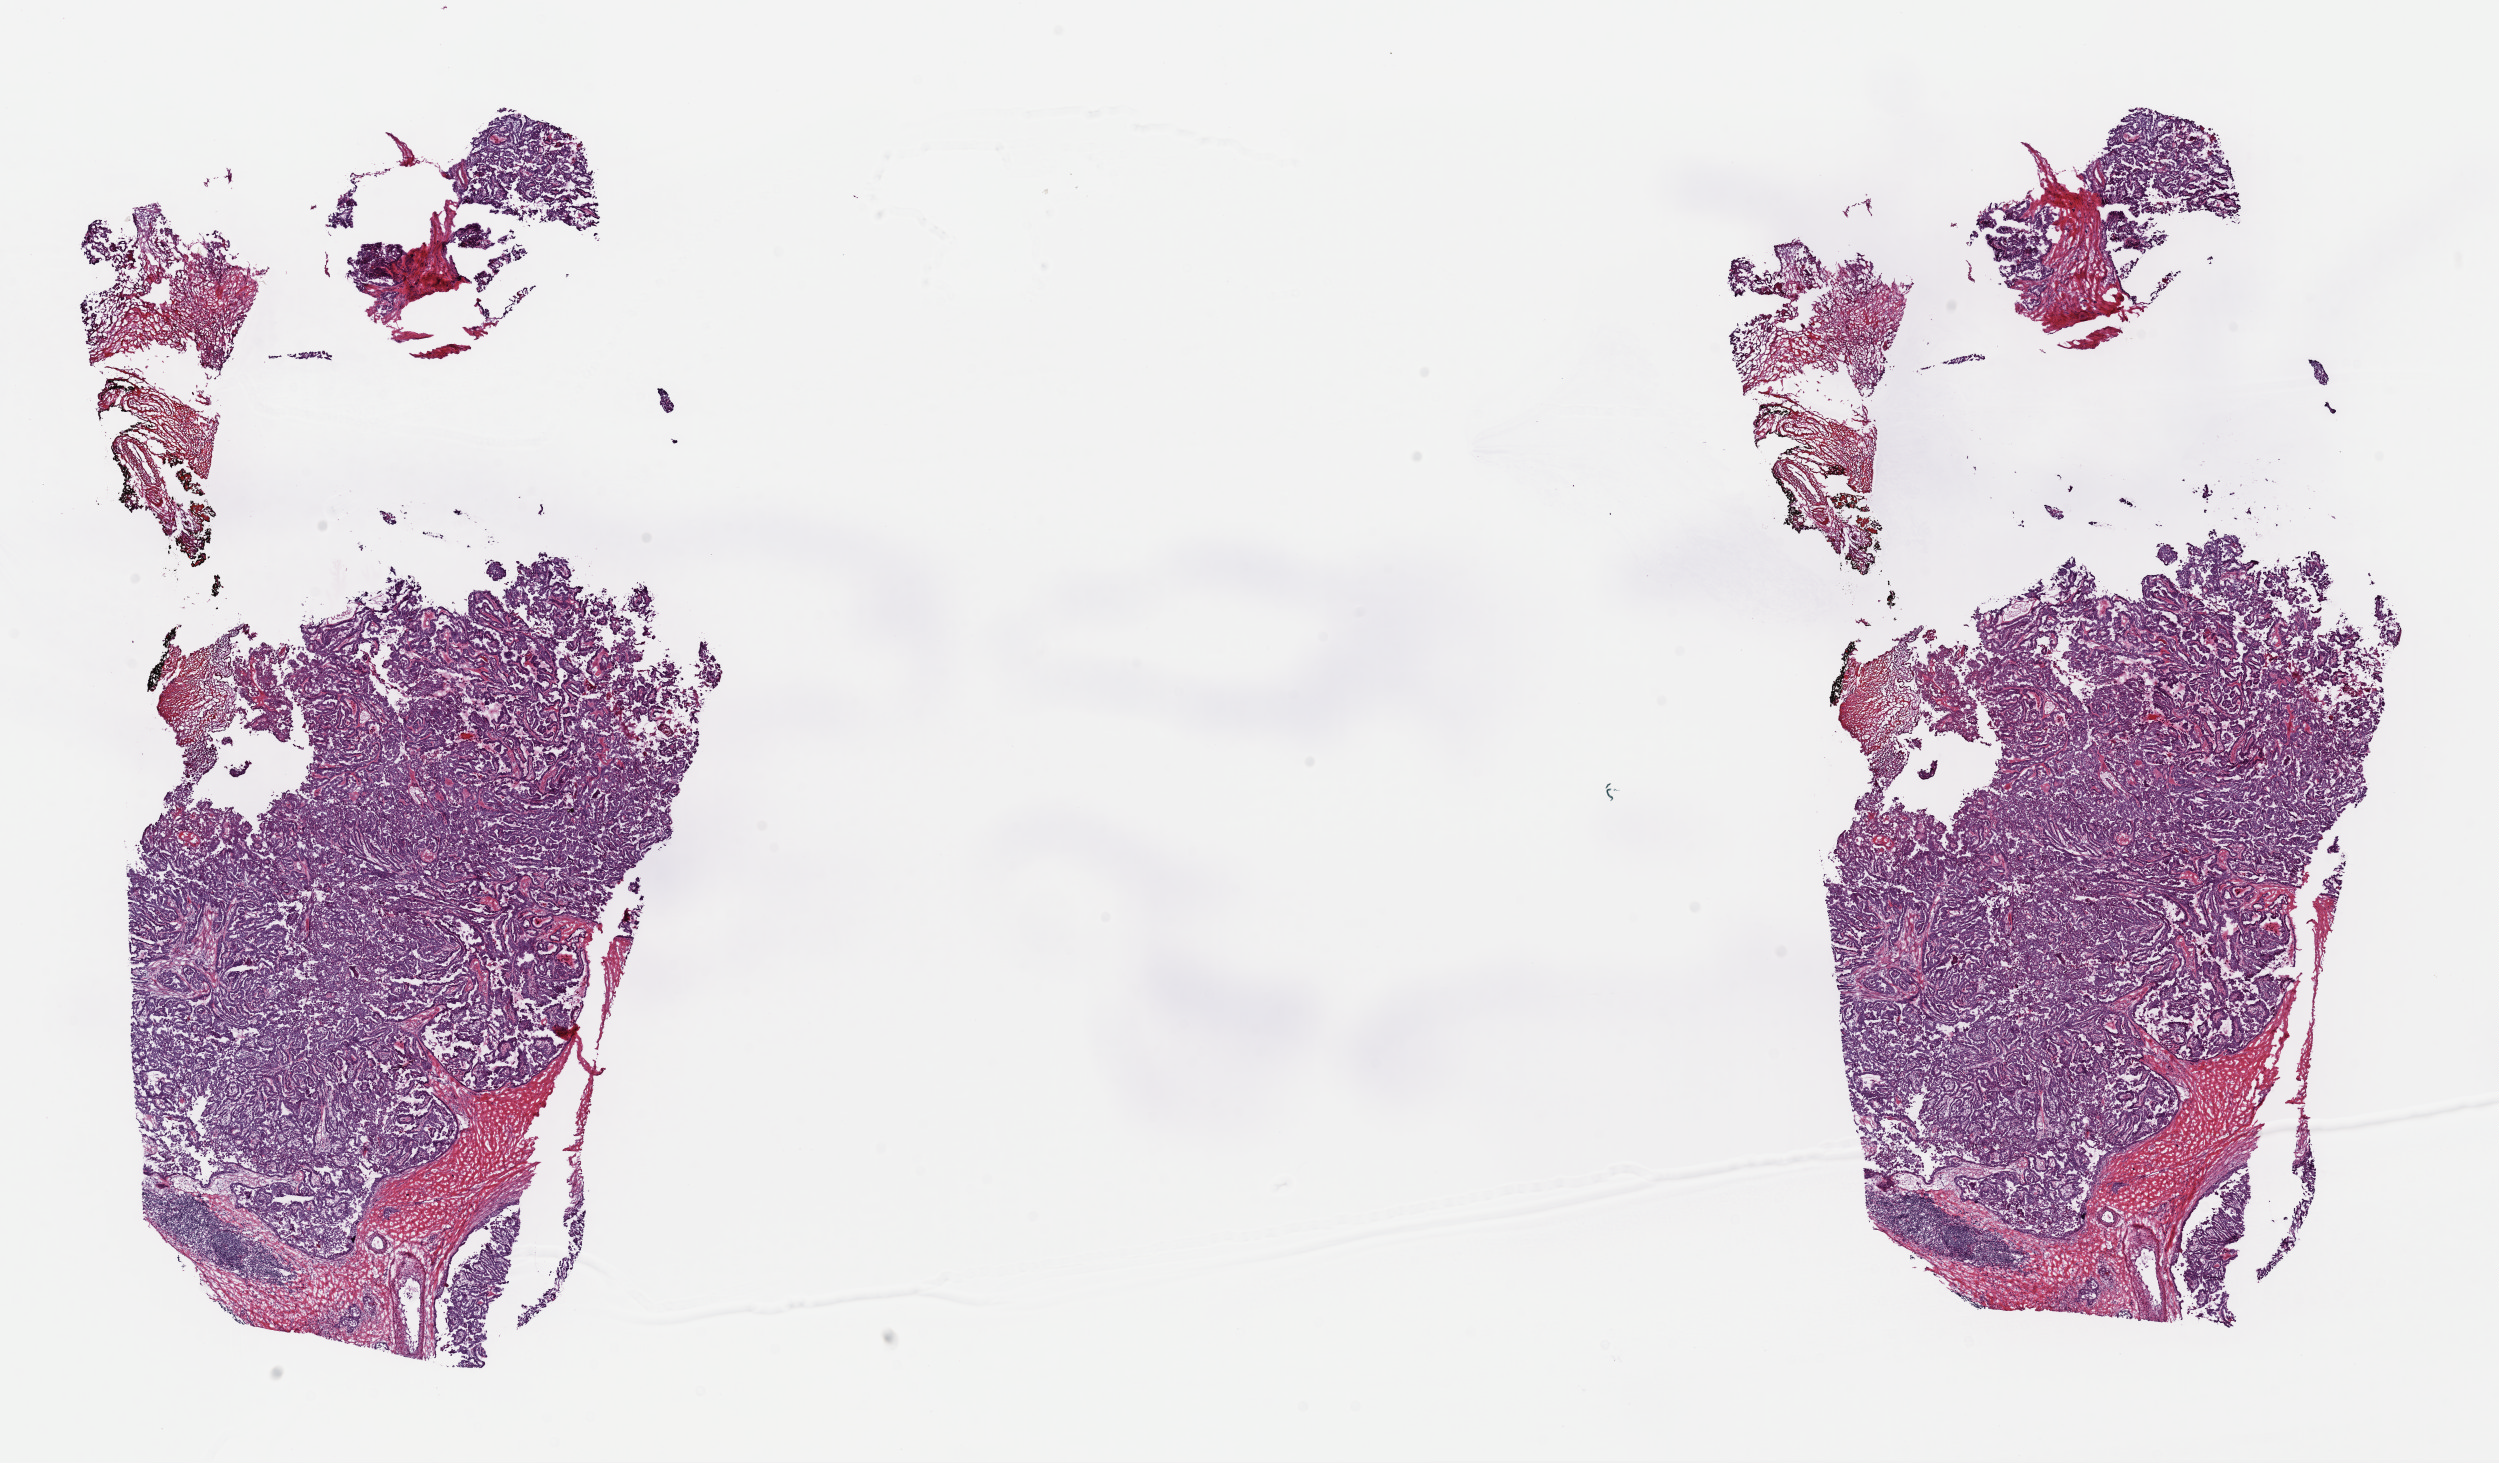
H&E-stained whole-slide image — a low-resolution overview of the entire scanned area, about 19.7 x 11.6 mm (from a 40x scan); frozen section from the top of the tissue portion; primary tumour sample from the thyroid. Female, age 56 years at initial diagnosis. Pathologist review of this section (percent, as recorded): tumour cells 90%, tumour nuclei 85%, normal cells 0%, stromal cells 10%, necrosis 0%. Inflammatory infiltration, as recorded: lymphocyte infiltration 0%, monocyte infiltration 0%, neutrophil infiltration 0%.
Histologic diagnosis: Papillary carcinoma, columnar cell (thyroid gland). AJCC pathologic stage: III (6th edition).